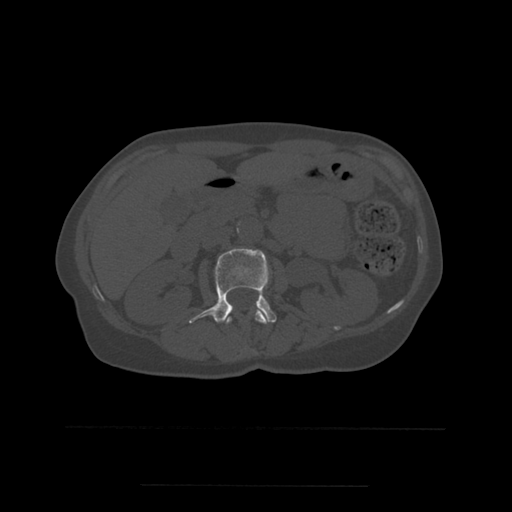
CT including the spine, one axial slice; position 219 of 544 along the scan axis; bone window (W 1800 / L 400 HU); 1.25 mm slice thickness; 512 × 512 image matrix, field of view 350 × 350 mm. Patient age 58 years. Case-level facts recorded for this patient, not image findings: primary cancer: lung.
Structures marked on this image (semi-automatically segmented with operator editing):
- L1 vertebra: bounding box <226,310,268,324> (left, top, right, bottom; pixels)
- L2 vertebra: <189,248,277,324>